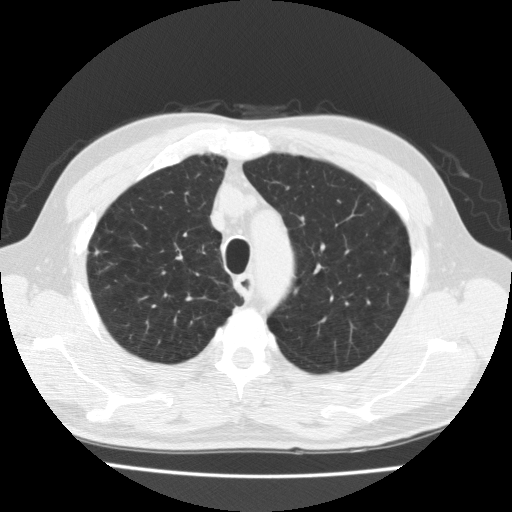
Low-dose screening chest CT, one axial slice; slice 169 of 205 in the series (ordered by position); reconstruction kernel FC10; lung window (W 1500 / L -600 HU); 2 mm slice thickness; 512 × 512 image matrix, field of view 350 × 350 mm.
Outlined on this slice (expert manual segmentation):
- lesion 1 (tumor, upper lobe of right lung): box from (x=95, y=248) to (x=103, y=256) px